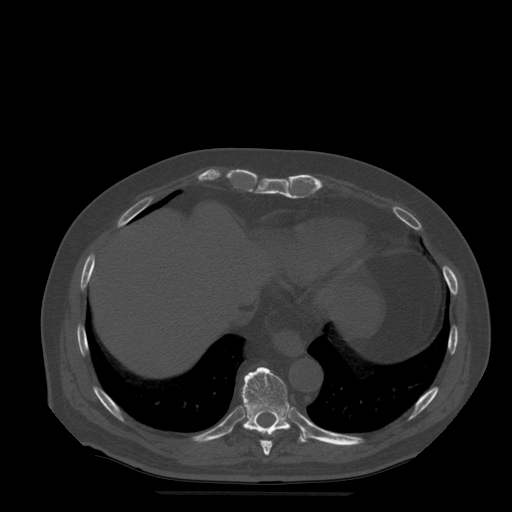
CT including the spine, one axial slice; position 276 of 522 along the scan axis; bone window (W 1800 / L 400 HU); 512 × 512 image matrix. Patient age 72 years. From the clinical record (not read from this slice): primary cancer: prostate.
Outlined on this slice (semi-automatically segmented with operator editing):
- T10 vertebra: box from (x=242, y=367) to (x=308, y=443) px
- T9 vertebra: (x=260, y=440)–(x=273, y=456)